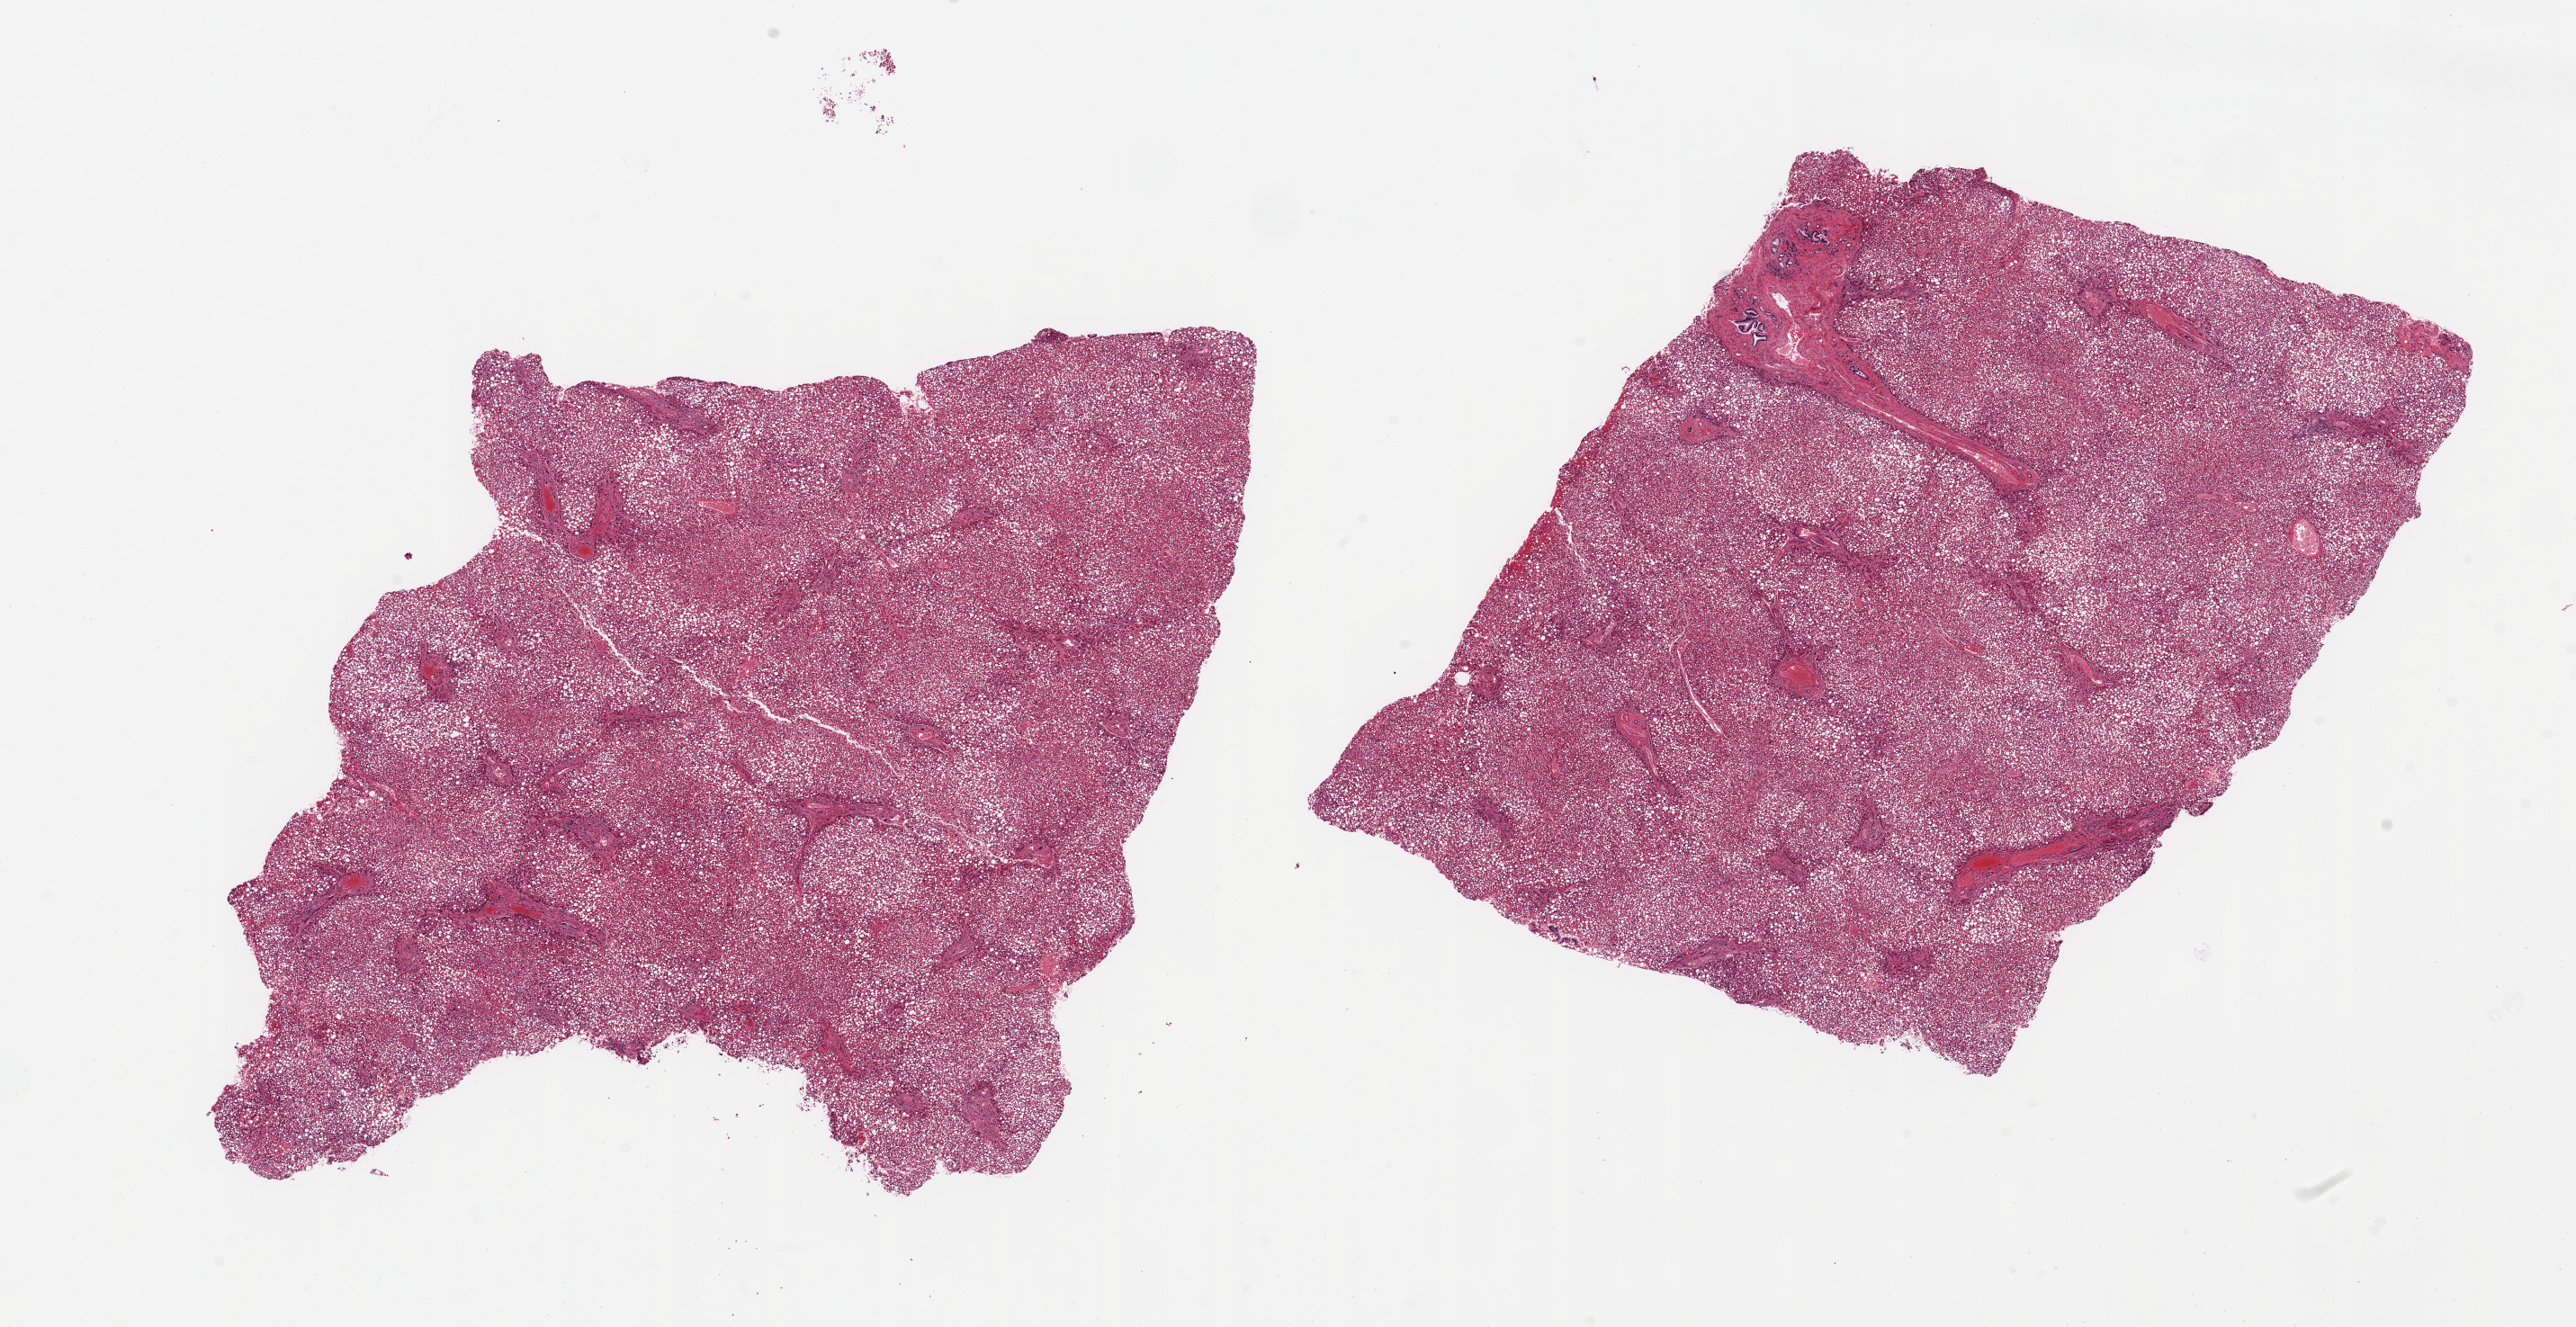
Digitized H&E-stained section — low-resolution overview of the scanned area, about 22.6 x 11.7 mm; PAXgene-fixed, paraffin-embedded tissue; section of liver (target tissue); donor tissue sample. Donor: female.
Pathologist's review note for this sample: 2 pieces; severe macrovesicular steatosis.